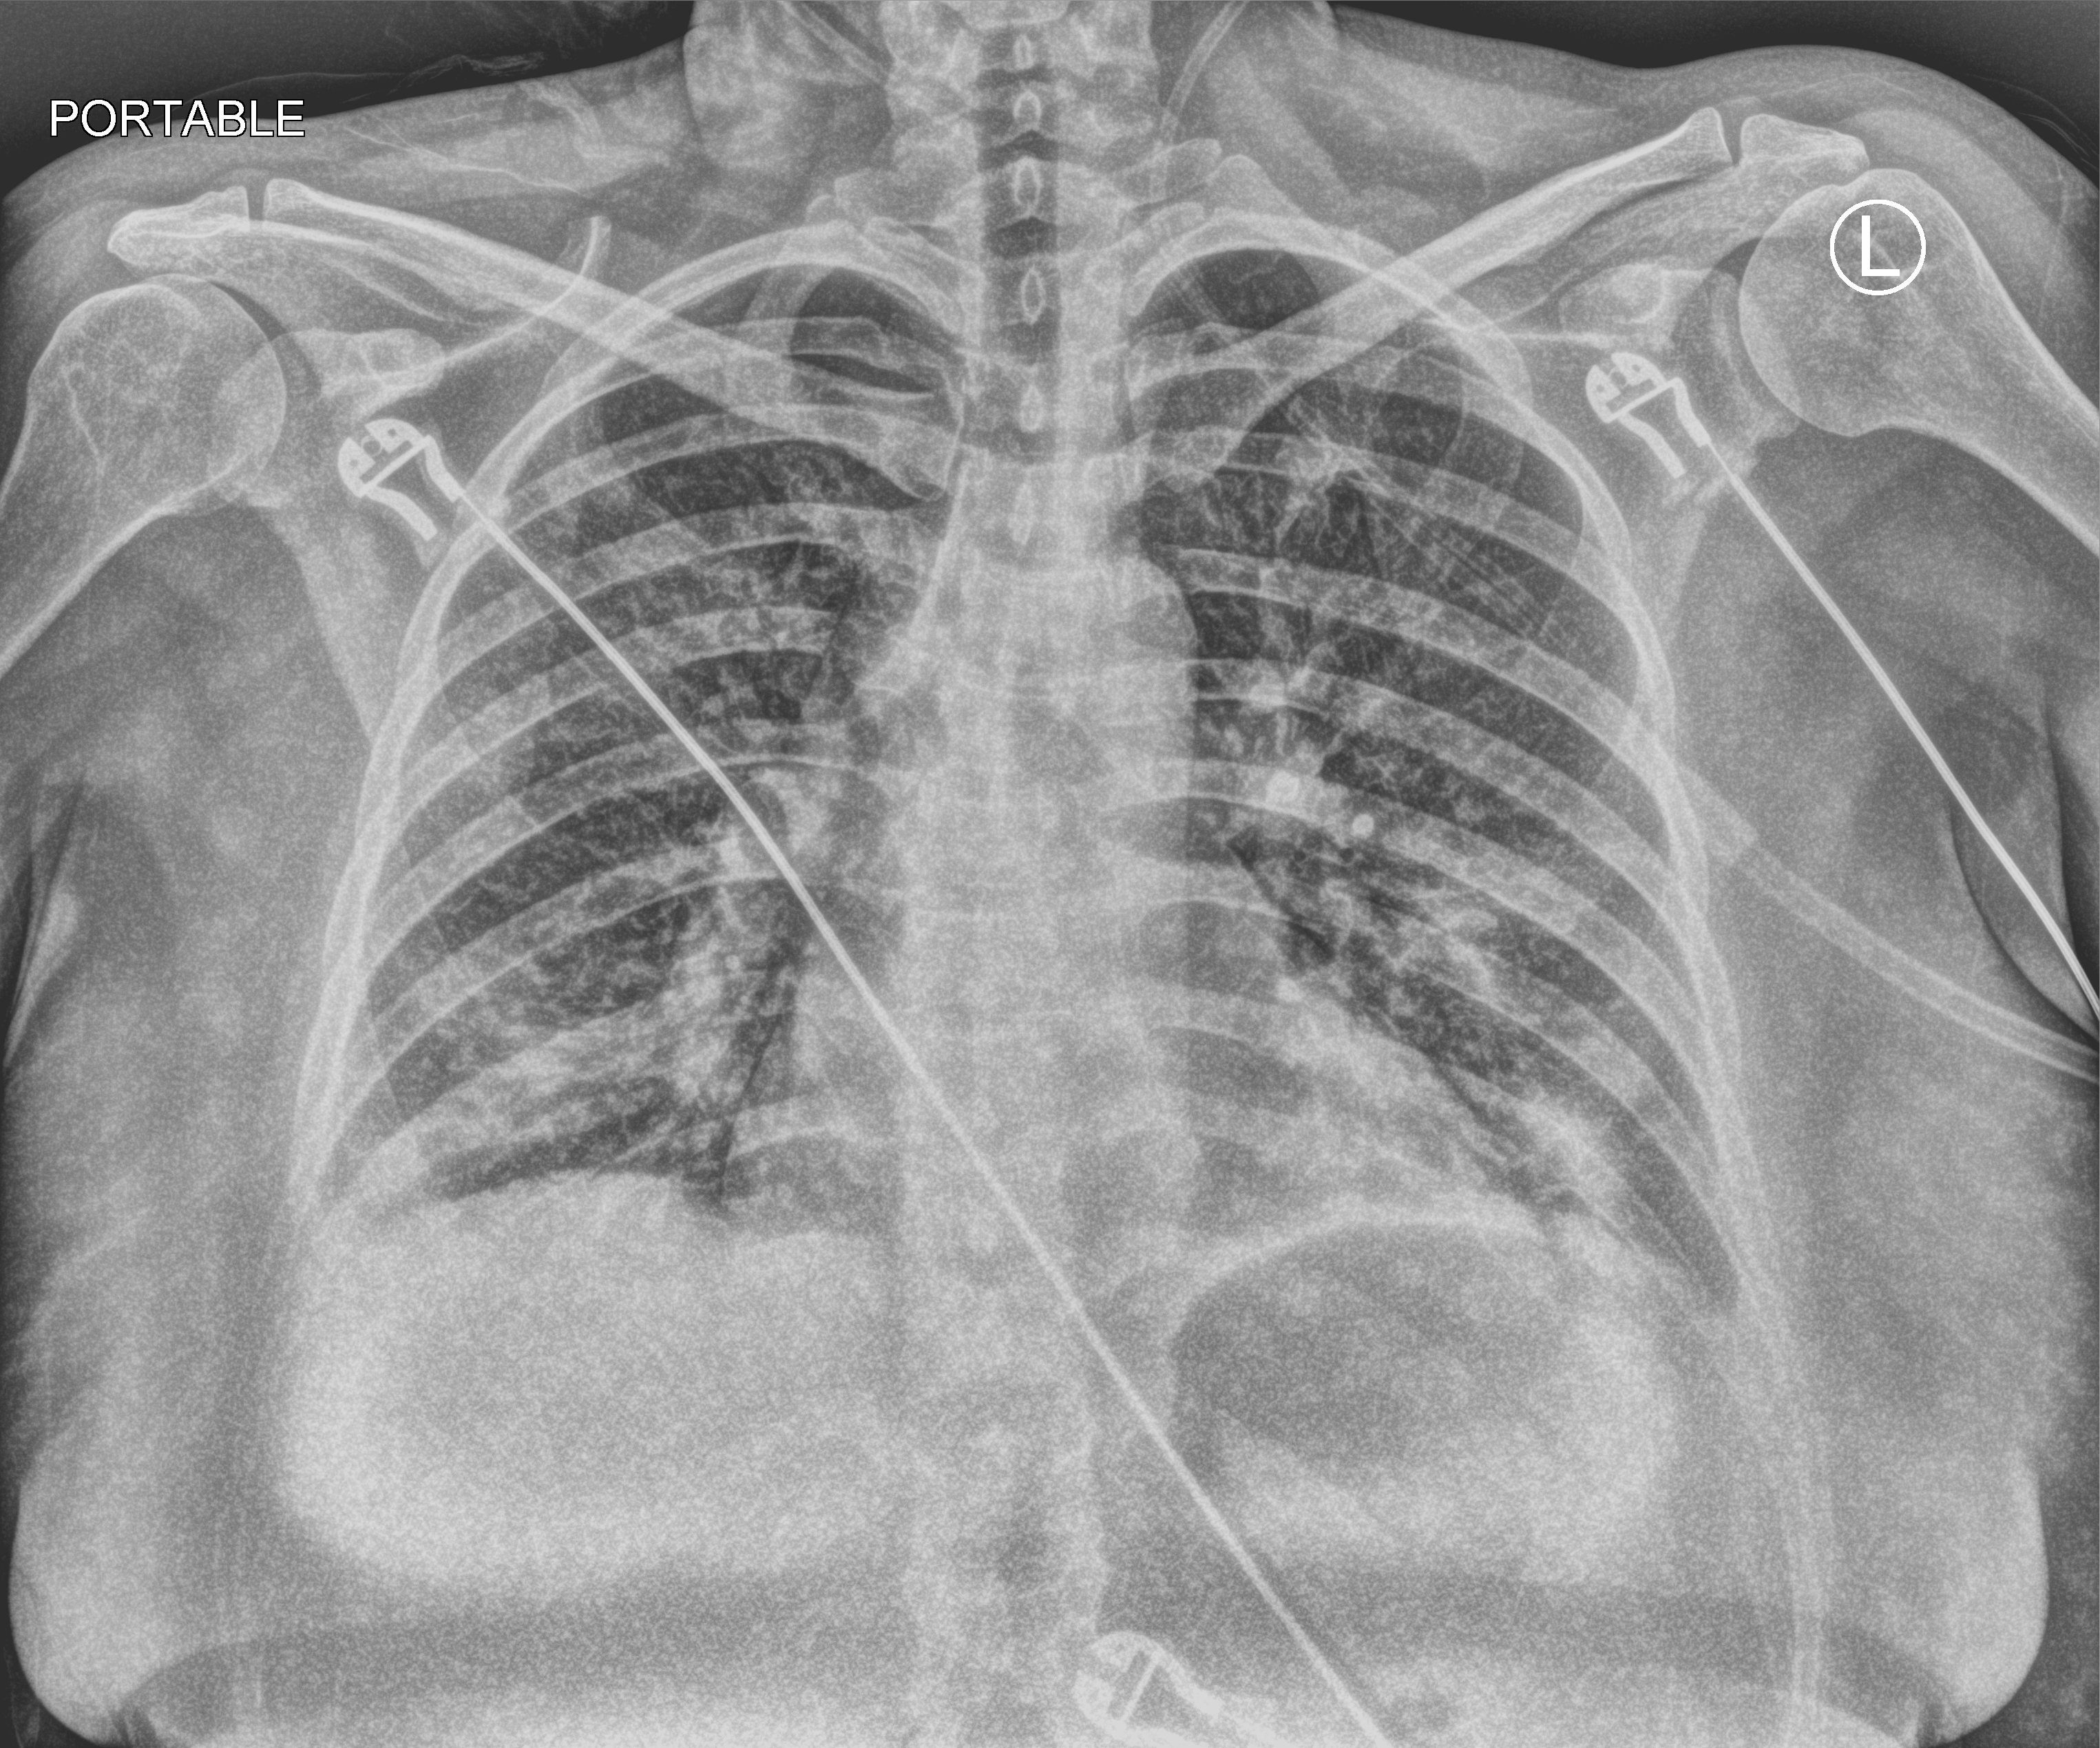
Chest X-ray (portable), anteroposterior (AP) projection. Patient hospitalised with COVID-19; female, aged 18–59 years.
From the hospital-stay record, not from the radiograph (when in the stay this image was taken is not recorded):
- admitted to intensive care during this hospital stay: no